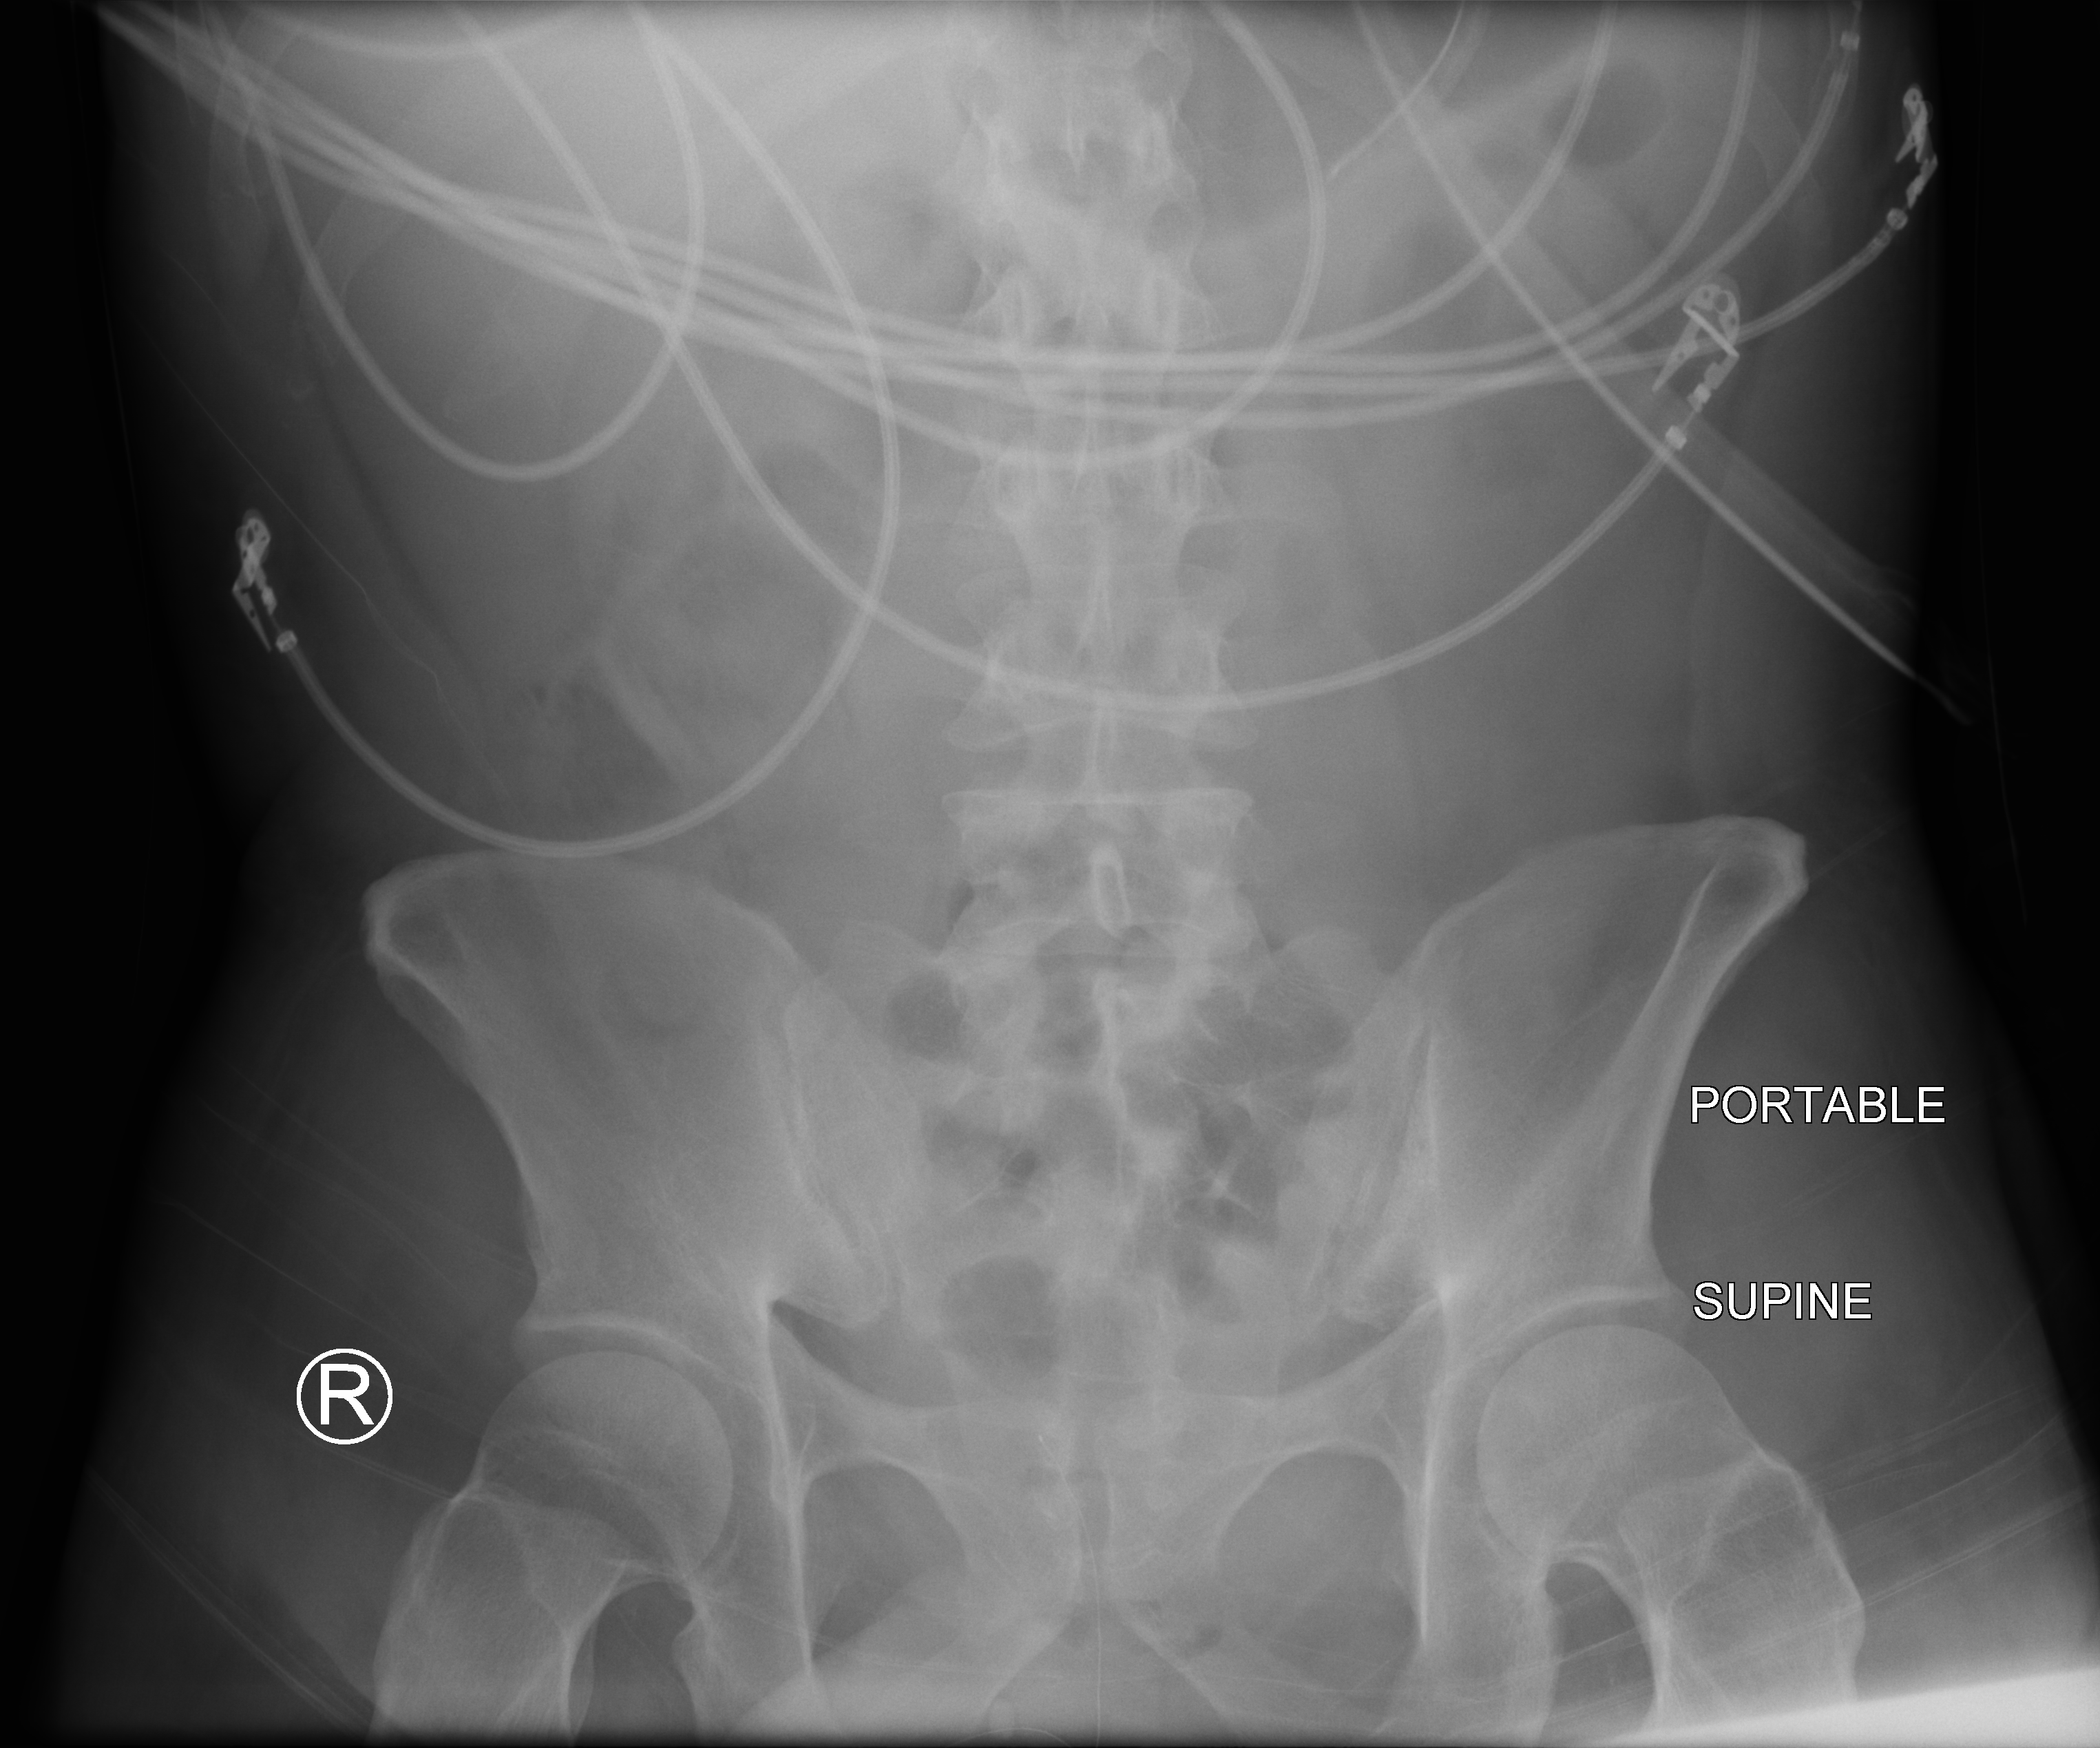
Bedside abdomen radiograph (computed radiography), anteroposterior (AP) projection. Patient hospitalised with COVID-19; male, aged 18–59 years.
Hospital-stay facts (about this admission, not read from this image; timing relative to this image not recorded):
- admitted to intensive care during this hospital stay: yes
- diabetes (admission record): yes
- mechanically ventilated during this hospital stay: yes